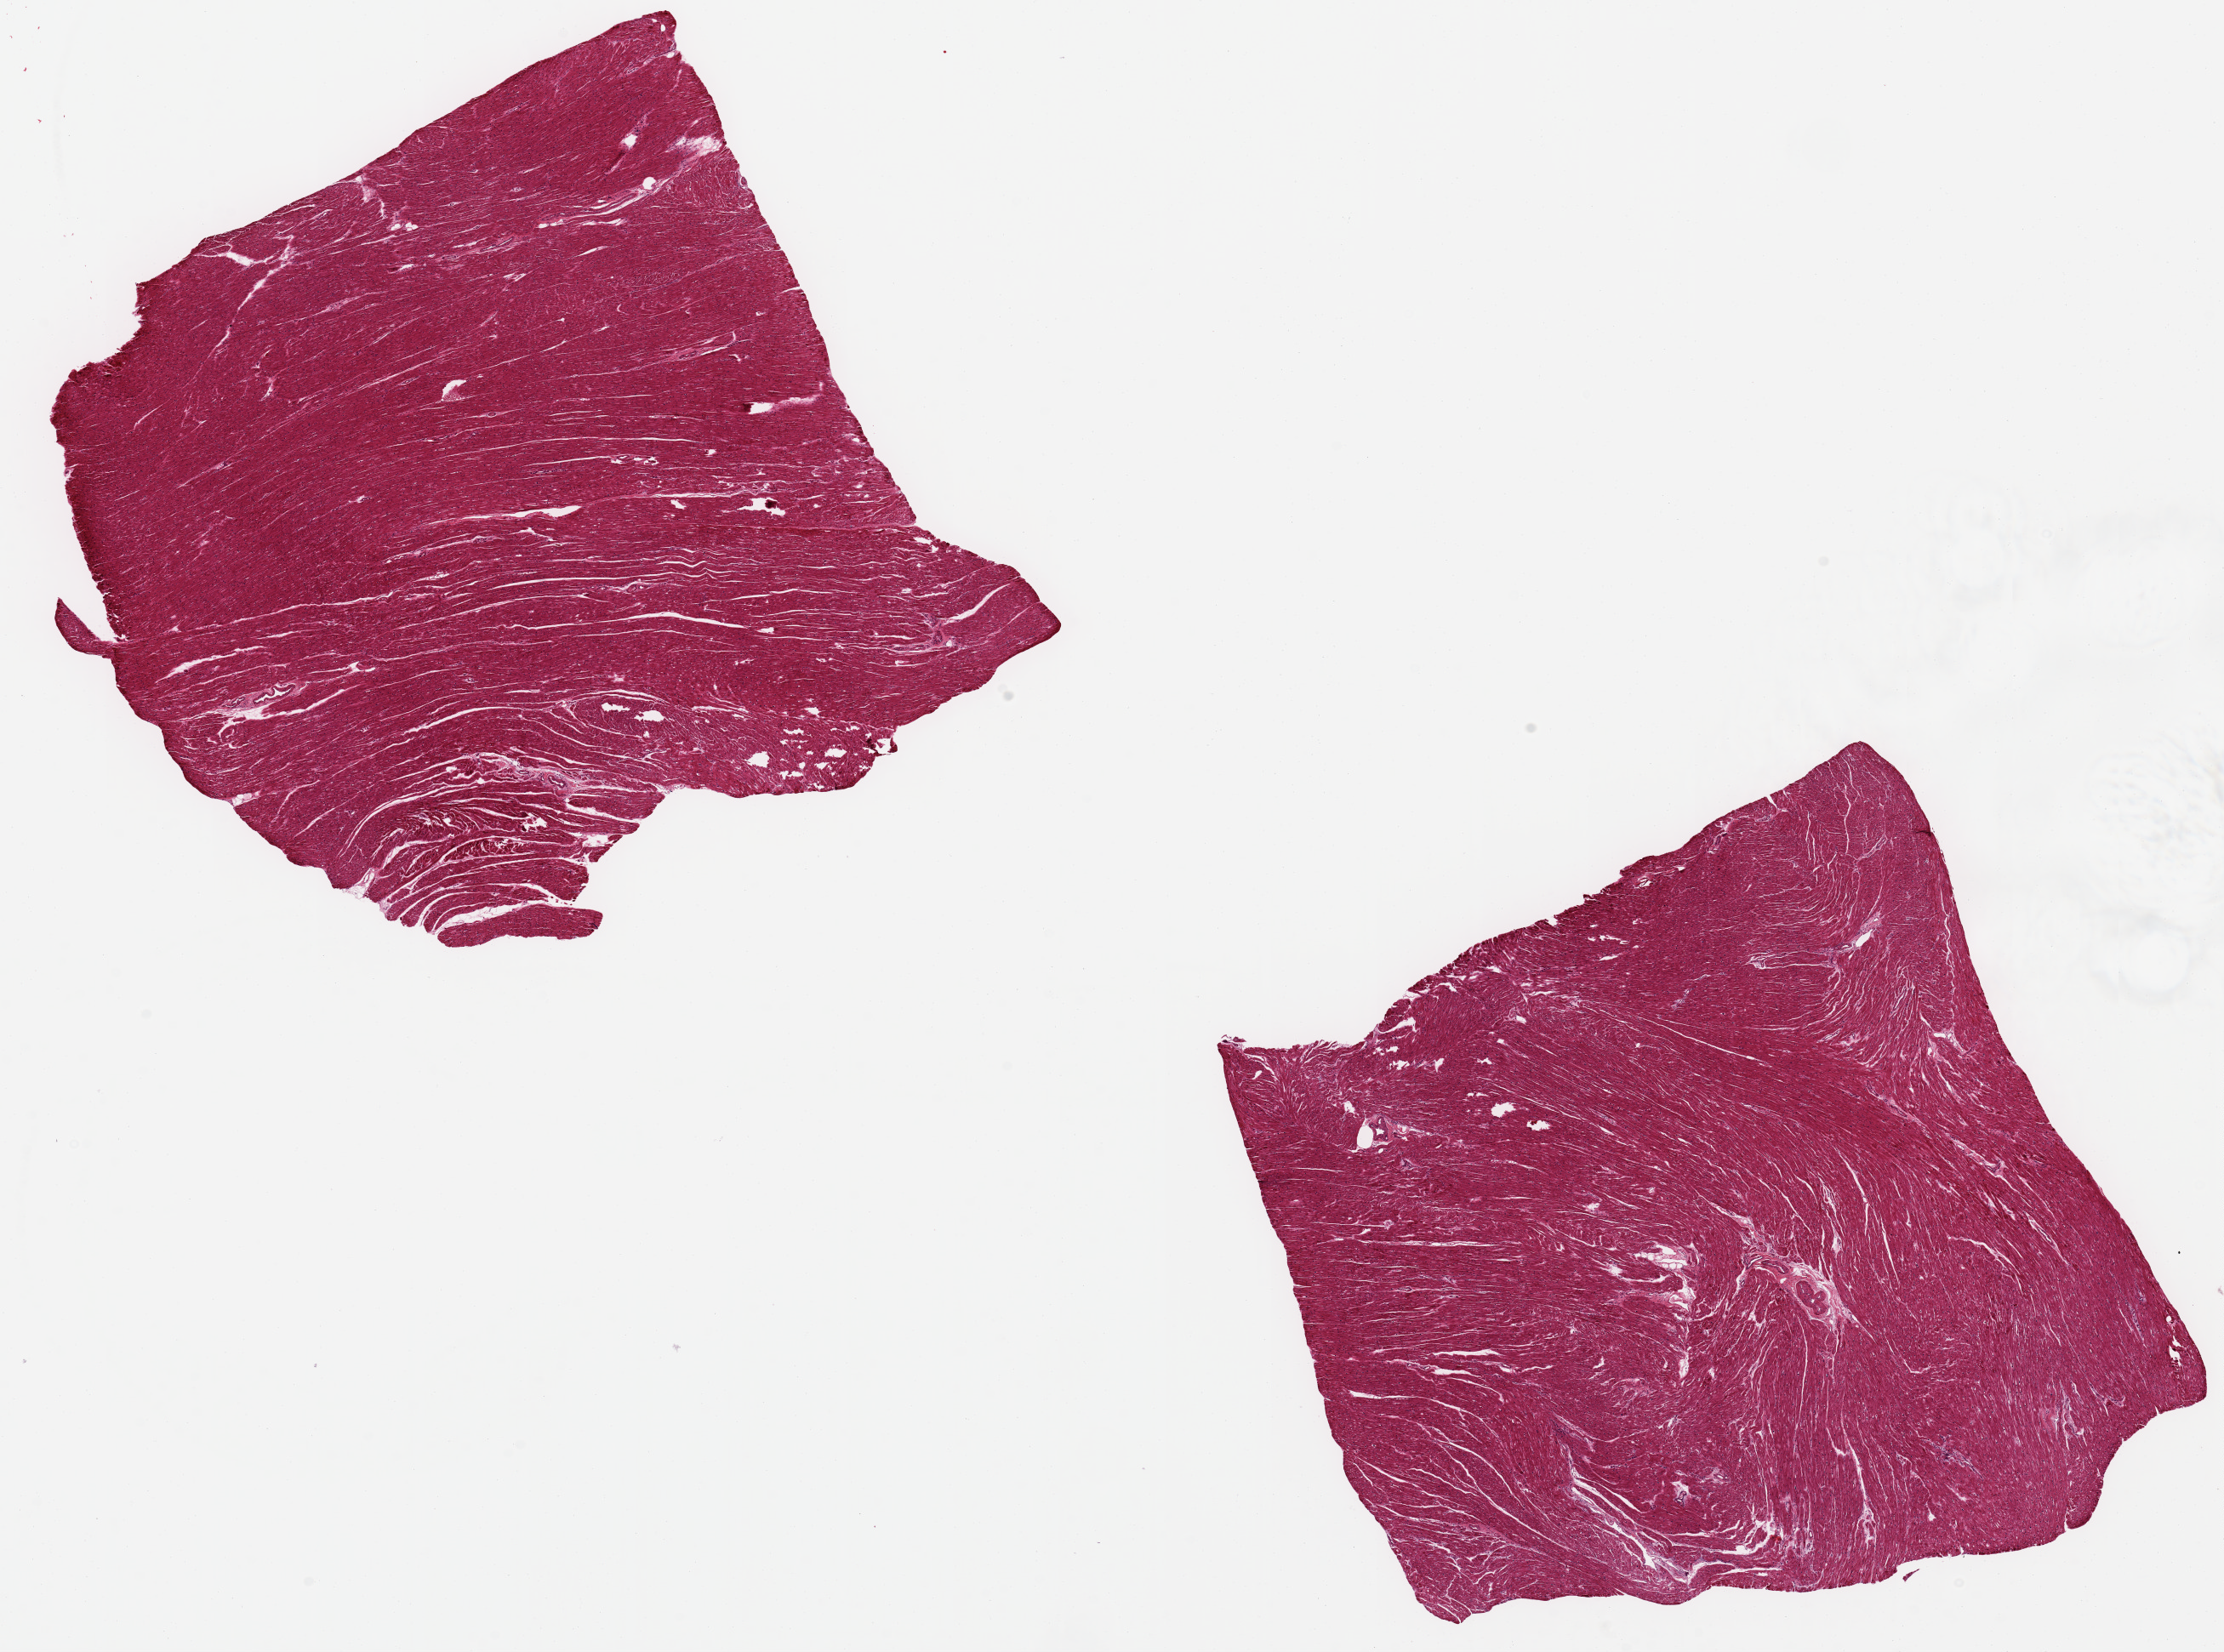
Digitized hematoxylin and eosin (H&E)-stained section, low-resolution overview of the scanned area, about 20.7 x 15.4 mm (acquisition: 20x scan); PAXgene-fixed, paraffin-embedded tissue; sampled site (target tissue): heart; donor tissue sample.
- review note (as recorded): 2 ~7x7mm pieces. Ischemic changes, numerous contraction bands noted